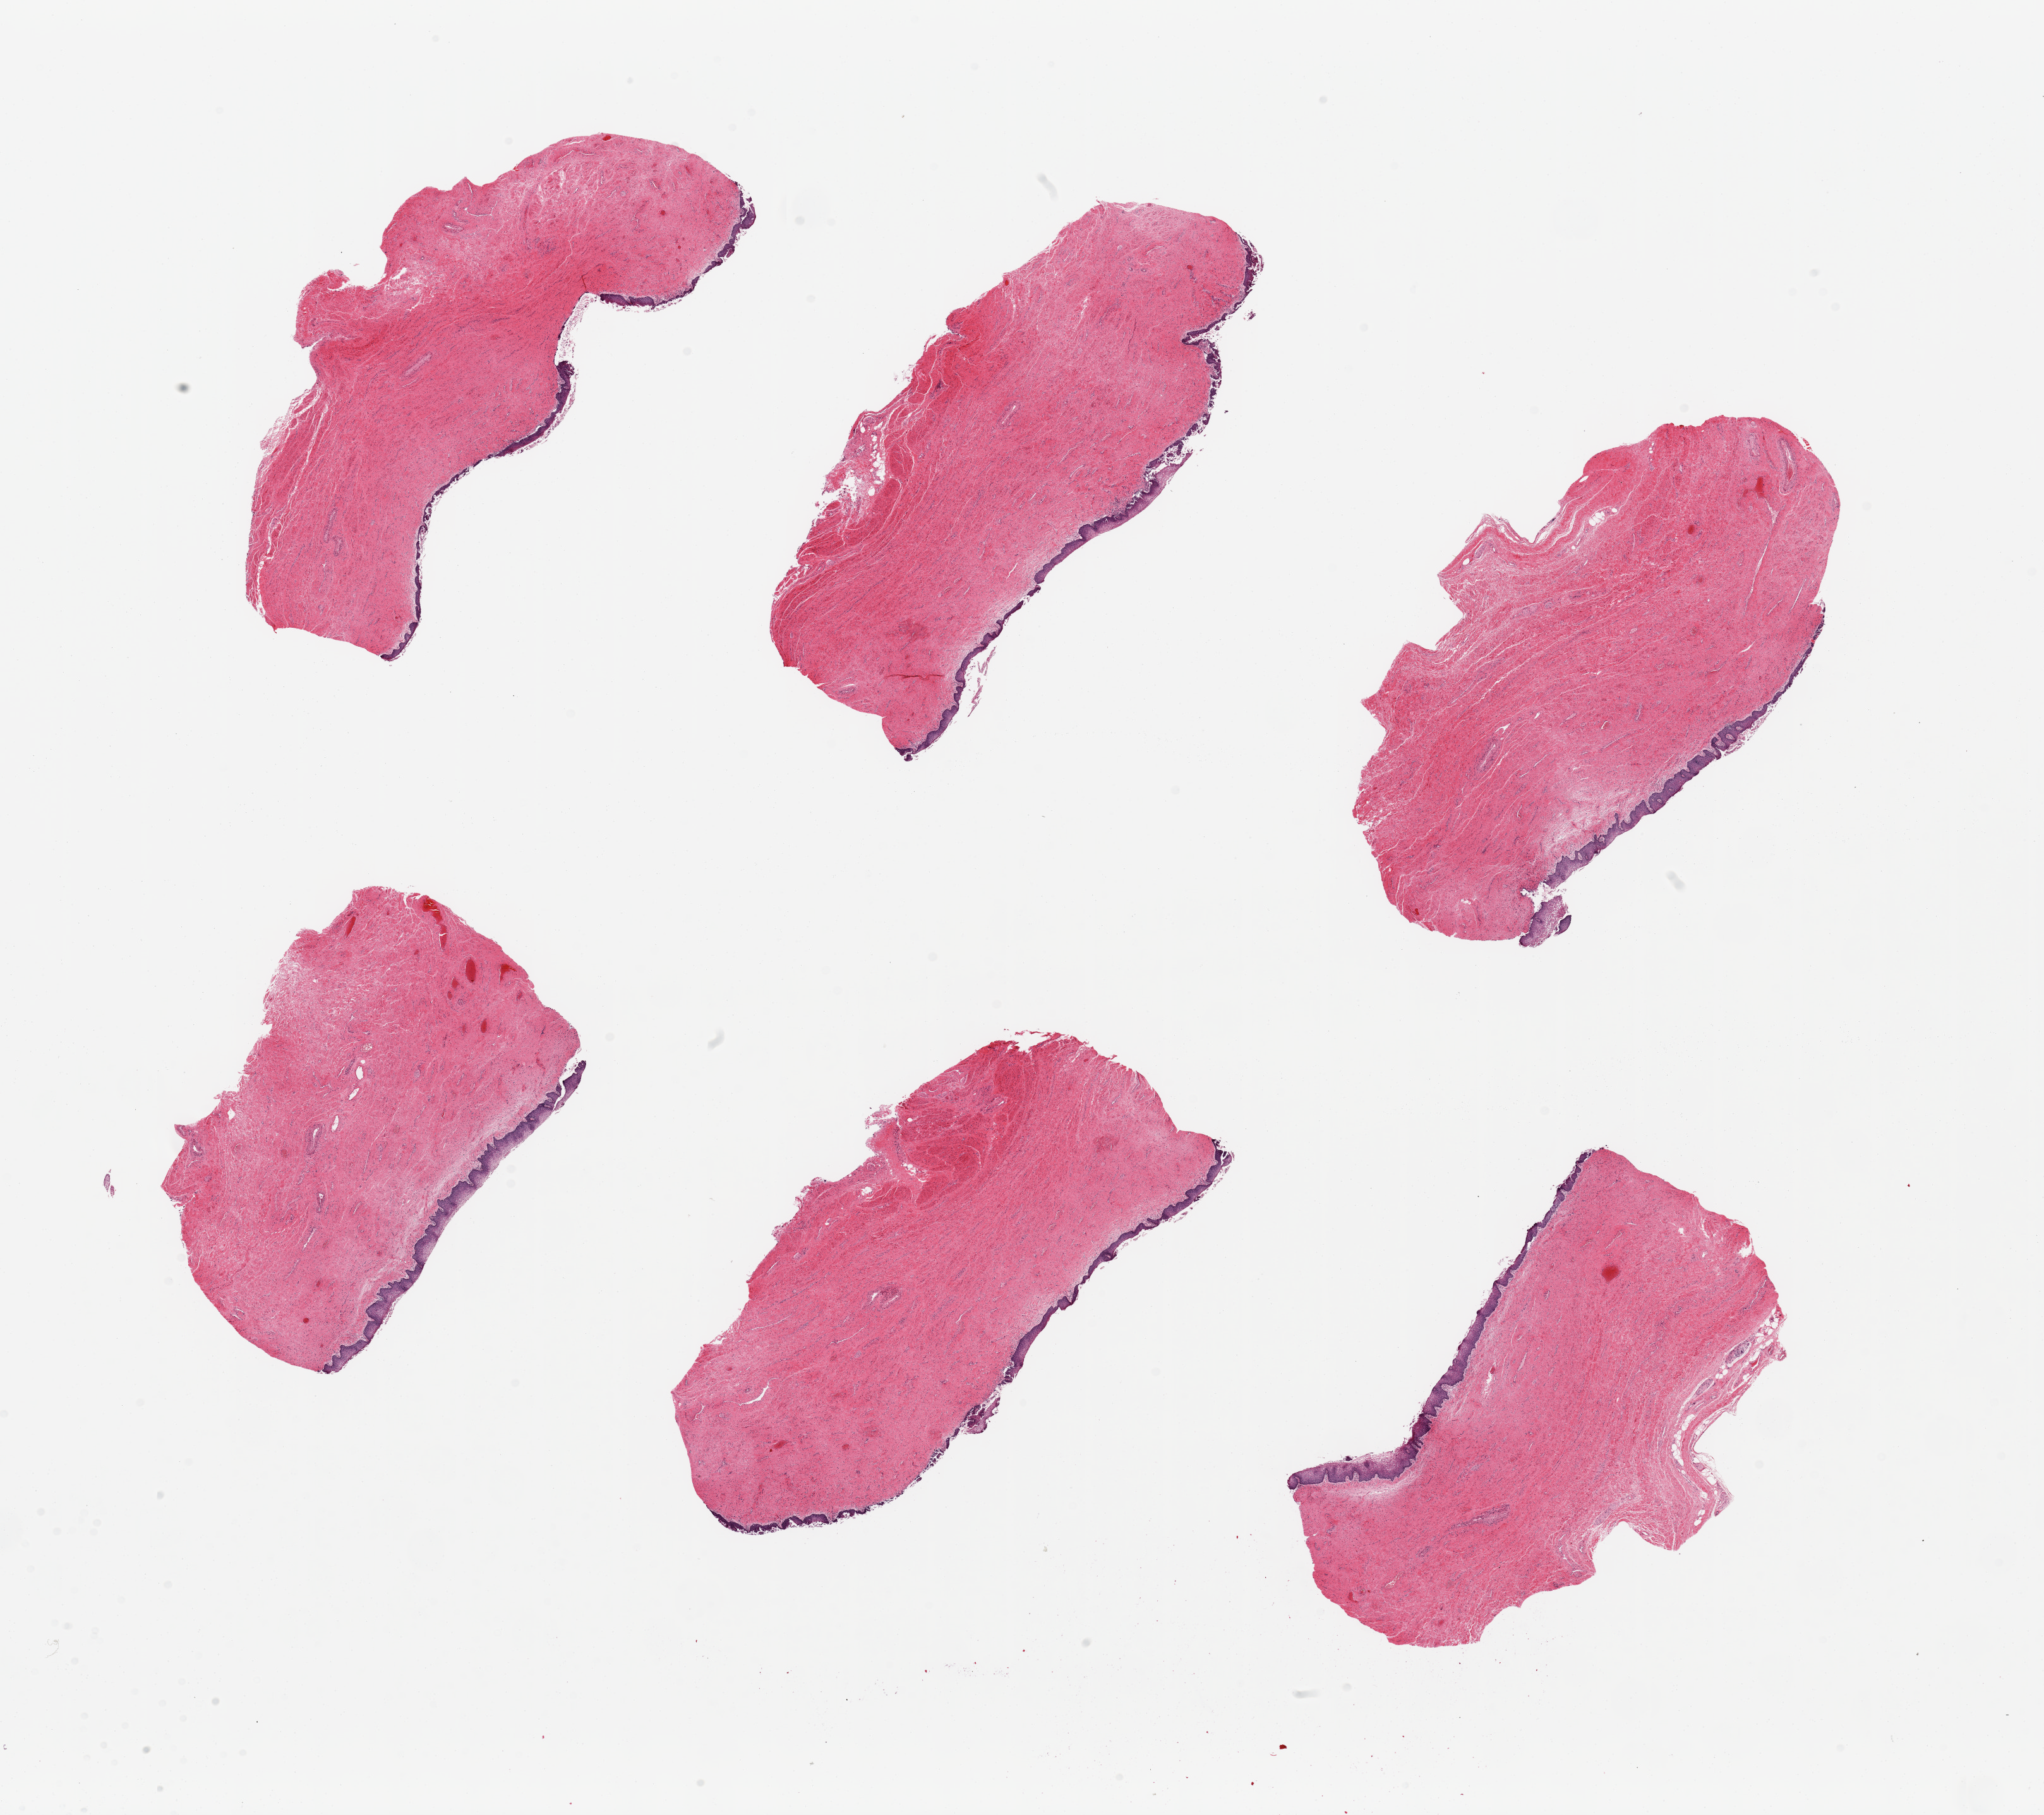
Whole-slide image, hematoxylin and eosin (H&E) stain, brightfield — a low-resolution overview of the entire scanned area, about 25.6 x 22.7 mm (from a 20x scan); PAXgene-fixed, paraffin-embedded tissue; section of vagina (target tissue); tissue donor sample. Female donor.
Pathologist's review note for this sample: 6 pieces, partially denuded squamous epithelium.